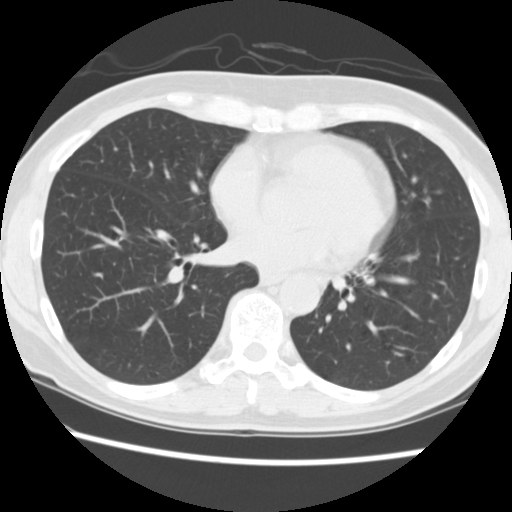
Low-dose screening chest CT, axial slice; second annual screen; lung window (W 1500 / L -600 HU); 2.5 mm slice thickness; 120 kVp. Female participant, aged 60 years at enrolment. Current smoker at enrolment.
Expert-annotated lung lesion, bounding box (x1, y1, x2, y2) in pixels: (411, 185, 450, 223). Screening reader's record for this exam: no non-calcified nodule ≥4 mm recorded. Official screen result: negative screen, minor abnormalities not suspicious for lung cancer. Lung cancer was diagnosed 509 days after this screen (after the third annual screen): adenocarcinoma, NOS, lingula, poorly differentiated (G3), stage IA (AJCC 6th edition), 6 mm at pathology.